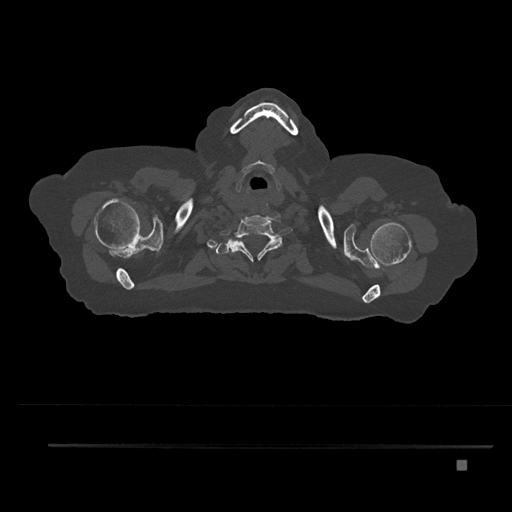
CT including the spine, one axial slice; slice 719 of 797 in the series (ordered by position); reconstruction kernel Br40s/3; 120 kVp; bone window (W 1800 / L 400 HU); 0.5 mm slice thickness; 512 × 512 image matrix. Female patient, age 76 years. Case-level facts recorded for this patient, not image findings: primary cancer: lung.
Outlined on this slice (semi-automatically segmented with operator editing):
- T1 vertebra: bounding box (x1, y1, x2, y2) in pixels: (222, 241, 252, 259)